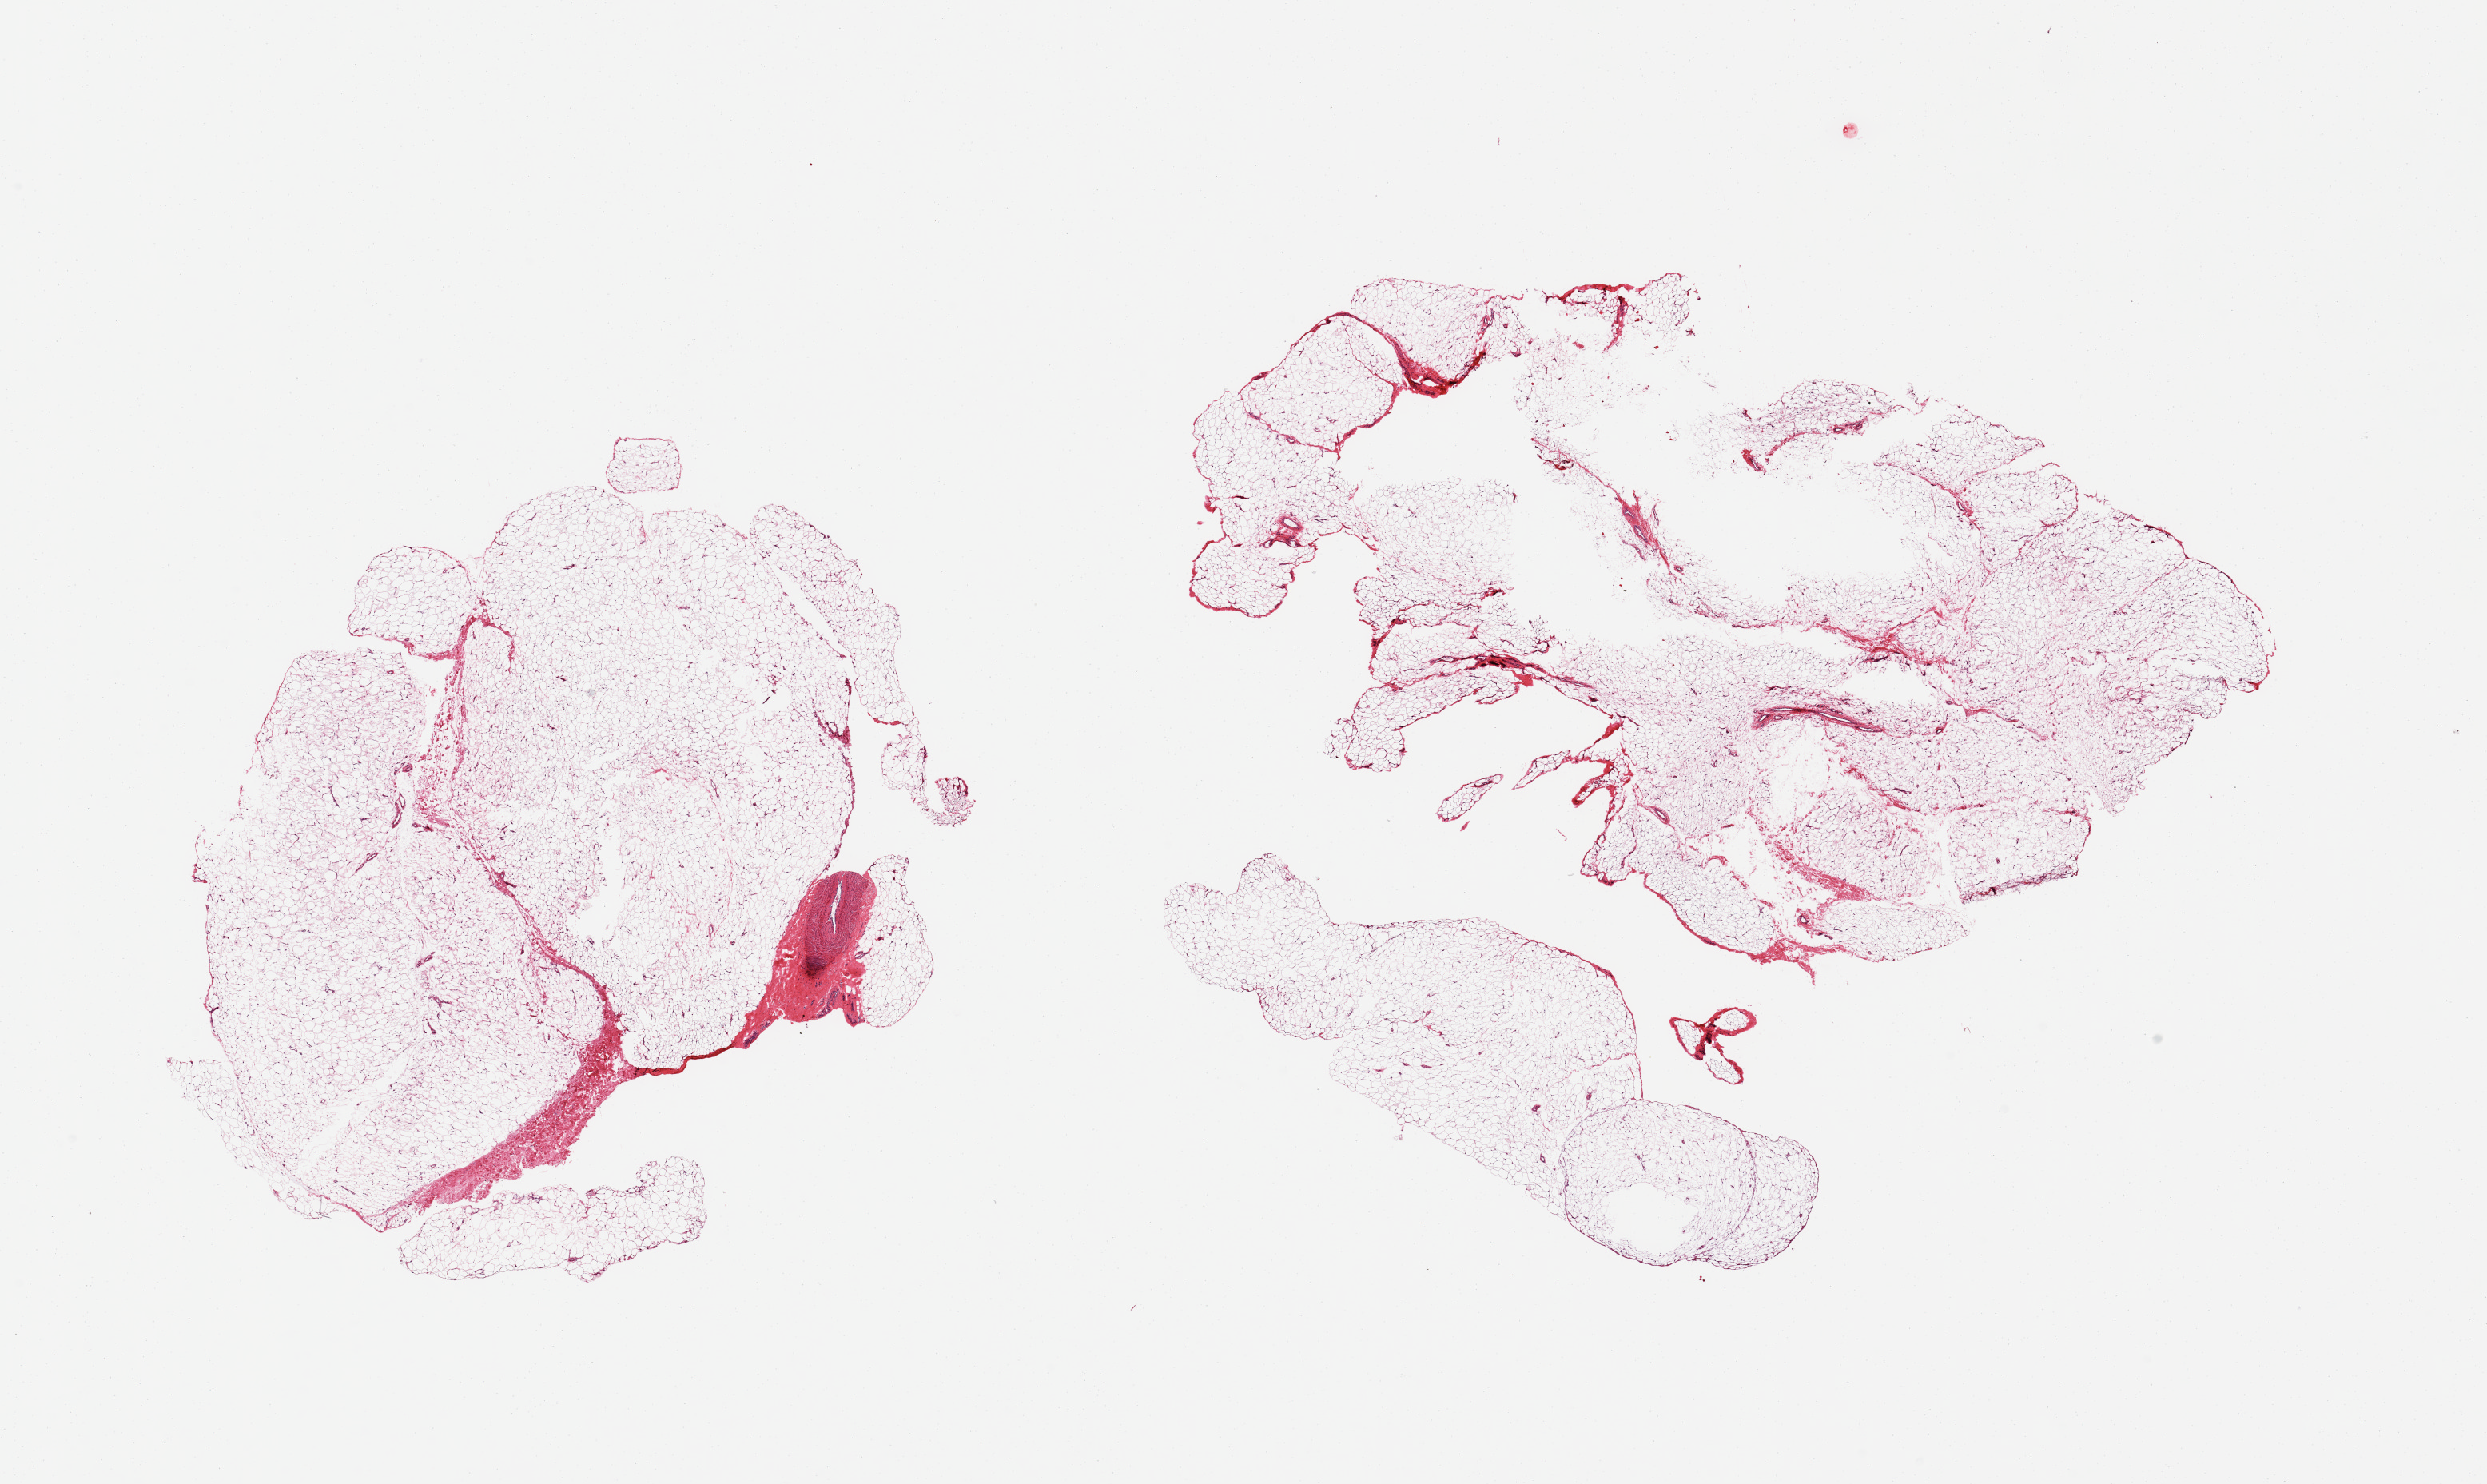
Whole-slide image, H&E stain, brightfield, low-resolution overview of the scanned area, about 24.6 x 14.7 mm (slide scanned at 20x), PAXgene-fixed, paraffin-embedded tissue, sampled site (target tissue): adipose tissue, tissue donor sample. Donor sex: male.
Review note (as recorded): 2 pieces, ~10% fascia/vascular elements.